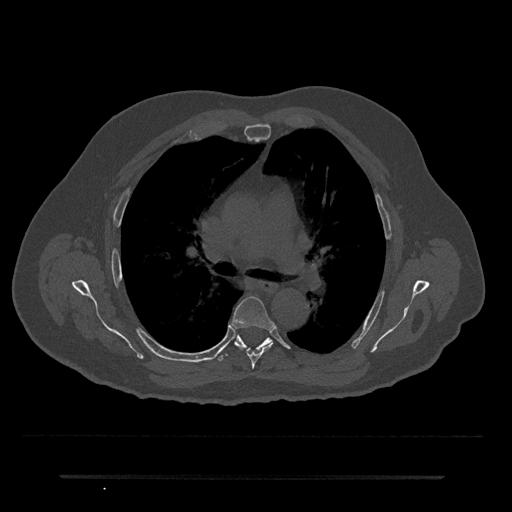
CT including the spine, one axial slice. Position 464 of 797 along the scan axis. 120 kVp. Bone window (W 1800 / L 400 HU). 0.5 mm slice thickness. 512 × 512 image matrix, field of view 437 × 437 mm. Patient: male, 69 years. Case-level facts recorded for this patient, not image findings: primary cancer: prostate.
Annotated regions visible in this slice (semi-automatically segmented with operator editing):
- T5 vertebra: box from (x=232, y=296) to (x=274, y=369) px
- T6 vertebra: (x=218, y=335)–(x=272, y=361)